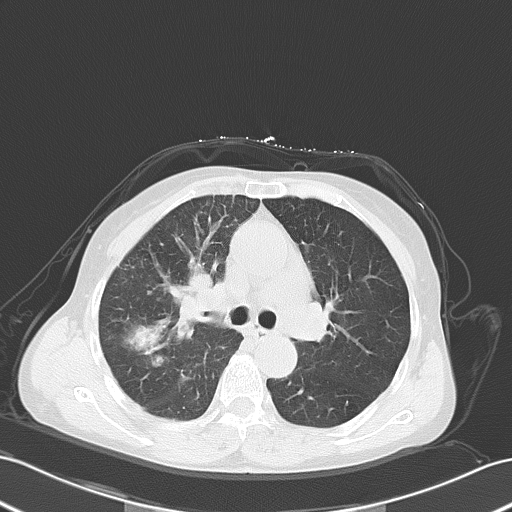
Chest CT, one axial slice. Slice 35 of 55 in the series (ordered by position). 120 kVp. Lung window (W 1500 / L -600 HU). 5 mm slice thickness. 512 × 512 image matrix, field of view 353 × 353 mm. Patient: female, 67 years. Case-level facts recorded for this patient, not image findings: clinical TNM (as recorded): T2a N3 M0; histopathological grade: G3.
Annotated regions visible in this slice (rectangle marked by the reading radiologist):
- lung tumour (recorded histology: small cell carcinoma): bounding box [x1, y1, x2, y2] px = [166, 259, 225, 336]